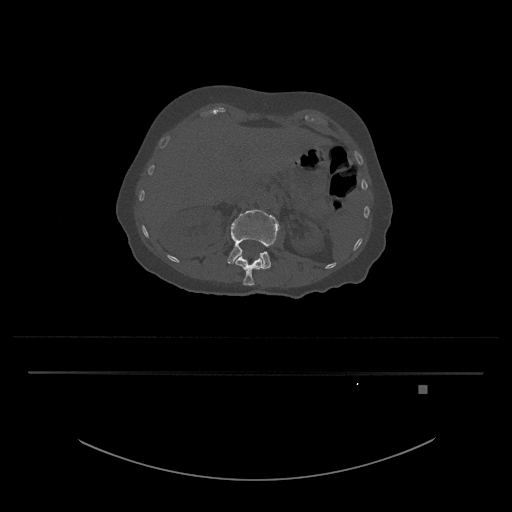
CT including the spine, one axial slice. Slice 520 of 797 in the series (ordered by position). Bone window (W 1800 / L 400 HU). 0.5 mm slice thickness. 512 × 512 image matrix, field of view 500 × 500 mm. Female patient, age 57 years. From the clinical record (not read from this slice): primary cancer: cervical.
Outlined on this slice (semi-automatically segmented with operator editing):
- L1 vertebra: bounding box <235,255,263,286> (left, top, right, bottom; pixels)